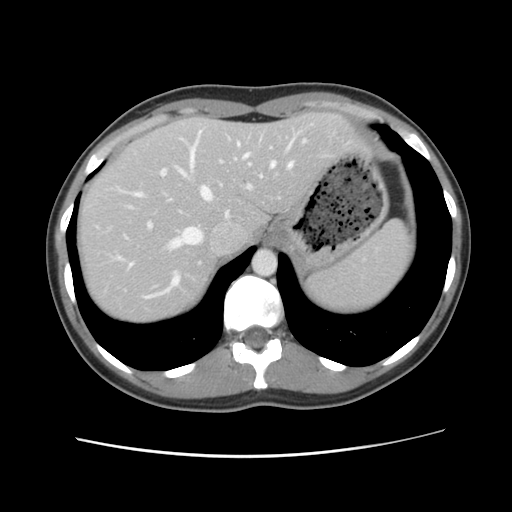
Contrast-enhanced abdominal CT, one axial slice; slice 92 of 134 in the series (ordered by position); 120 kVp; intravenous contrast given; soft-tissue window (W 400 / L 40 HU); 2.5 mm slice thickness; 512 × 512 image matrix, field of view 339 × 339 mm. Female patient, age 33 years. From the clinical record (not read from this slice): diagnosis: colorectal cancer liver metastases, imaged before liver resection; multiple liver metastases: yes; largest metastasis: 4.5 cm; chemotherapy before resection: no.
Outlined on this slice (outlined manually by an expert reader):
- hepatic veins: bounding box [x1, y1, x2, y2] px = [119, 132, 306, 297]
- liver: [77, 113, 365, 324]
- planned liver remnant (the part of the liver to remain after resection): [77, 114, 365, 324]
- portal vein (with intrahepatic branches): [125, 139, 273, 230]